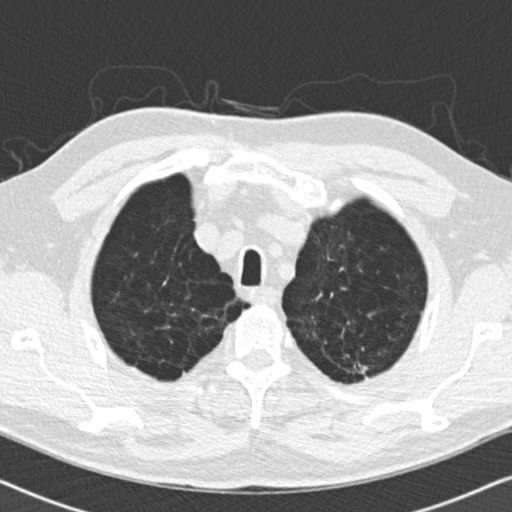
Low-dose screening chest CT, one axial slice. Position 152 of 175 along the scan axis. 120 kVp. Lung window (W 1500 / L -600 HU). 2 mm slice thickness. 512 × 512 image matrix, field of view 330 × 330 mm.
Annotated regions visible in this slice (manually delineated by an expert):
- lesion 1 (tumor, upper lobe of left lung): bounding box [x1, y1, x2, y2] px = [354, 364, 368, 373]